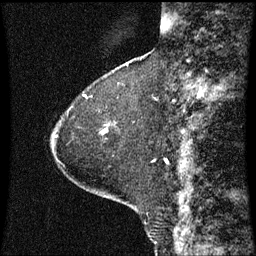
Breast MRI (dynamic contrast-enhanced), one sagittal slice; slice 19 of 60 in the series (ordered by position); dynamic contrast-enhanced series, image 2 of 3 at this slice position (ordered by acquisition); 1.5 T; TE 4.2 ms, TR 8.9 ms; 2 mm slice thickness; 256 × 256 image matrix, field of view 200 × 200 mm. Patient: female, 63 years. From the clinical record (not read from this slice): setting: breast cancer imaged before/during neoadjuvant chemotherapy; receptor status: HR-positive, HER2-negative.
Outlined on this slice (semi-automatic segmentation, software-assisted and operator-edited):
- analysis volume of interest (the breast-tissue region the enhancement analysis was run in; not a lesion): box from (x=101, y=130) to (x=106, y=135) px
- tumour enhancement mask (voxels above the 70 % enhancement threshold inside the analysis volume of interest): (x=102, y=130)–(x=106, y=133)